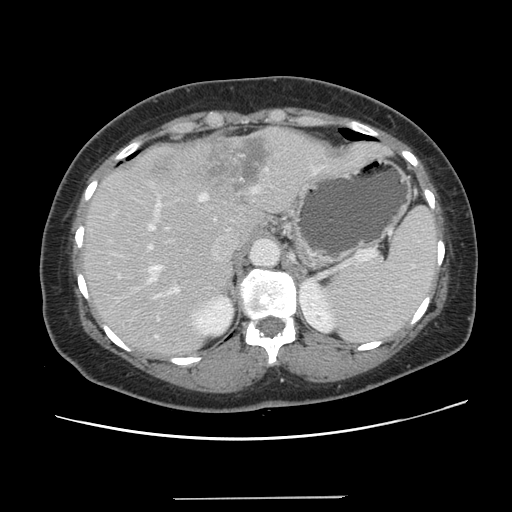
Contrast-enhanced abdominal CT, one axial slice; position 94 of 141 along the scan axis; intravenous contrast given; soft-tissue window (W 400 / L 40 HU); 2.5 mm slice thickness; 512 × 512 image matrix. Female patient, age 53 years. Case-level facts recorded for this patient, not image findings: diagnosis: colorectal cancer liver metastases, imaged before liver resection; multiple liver metastases: no; largest metastasis: 14.5 cm; disease in both lobes: yes.
Structures marked on this image (manually delineated by an expert):
- hepatic veins: box from (x=147, y=169) to (x=315, y=282) px
- liver: (x=84, y=129)–(x=387, y=355)
- planned liver remnant (the part of the liver to remain after resection): (x=84, y=209)–(x=262, y=355)
- portal vein (with intrahepatic branches): (x=147, y=187)–(x=258, y=321)
- liver metastasis: (x=160, y=140)–(x=269, y=193)